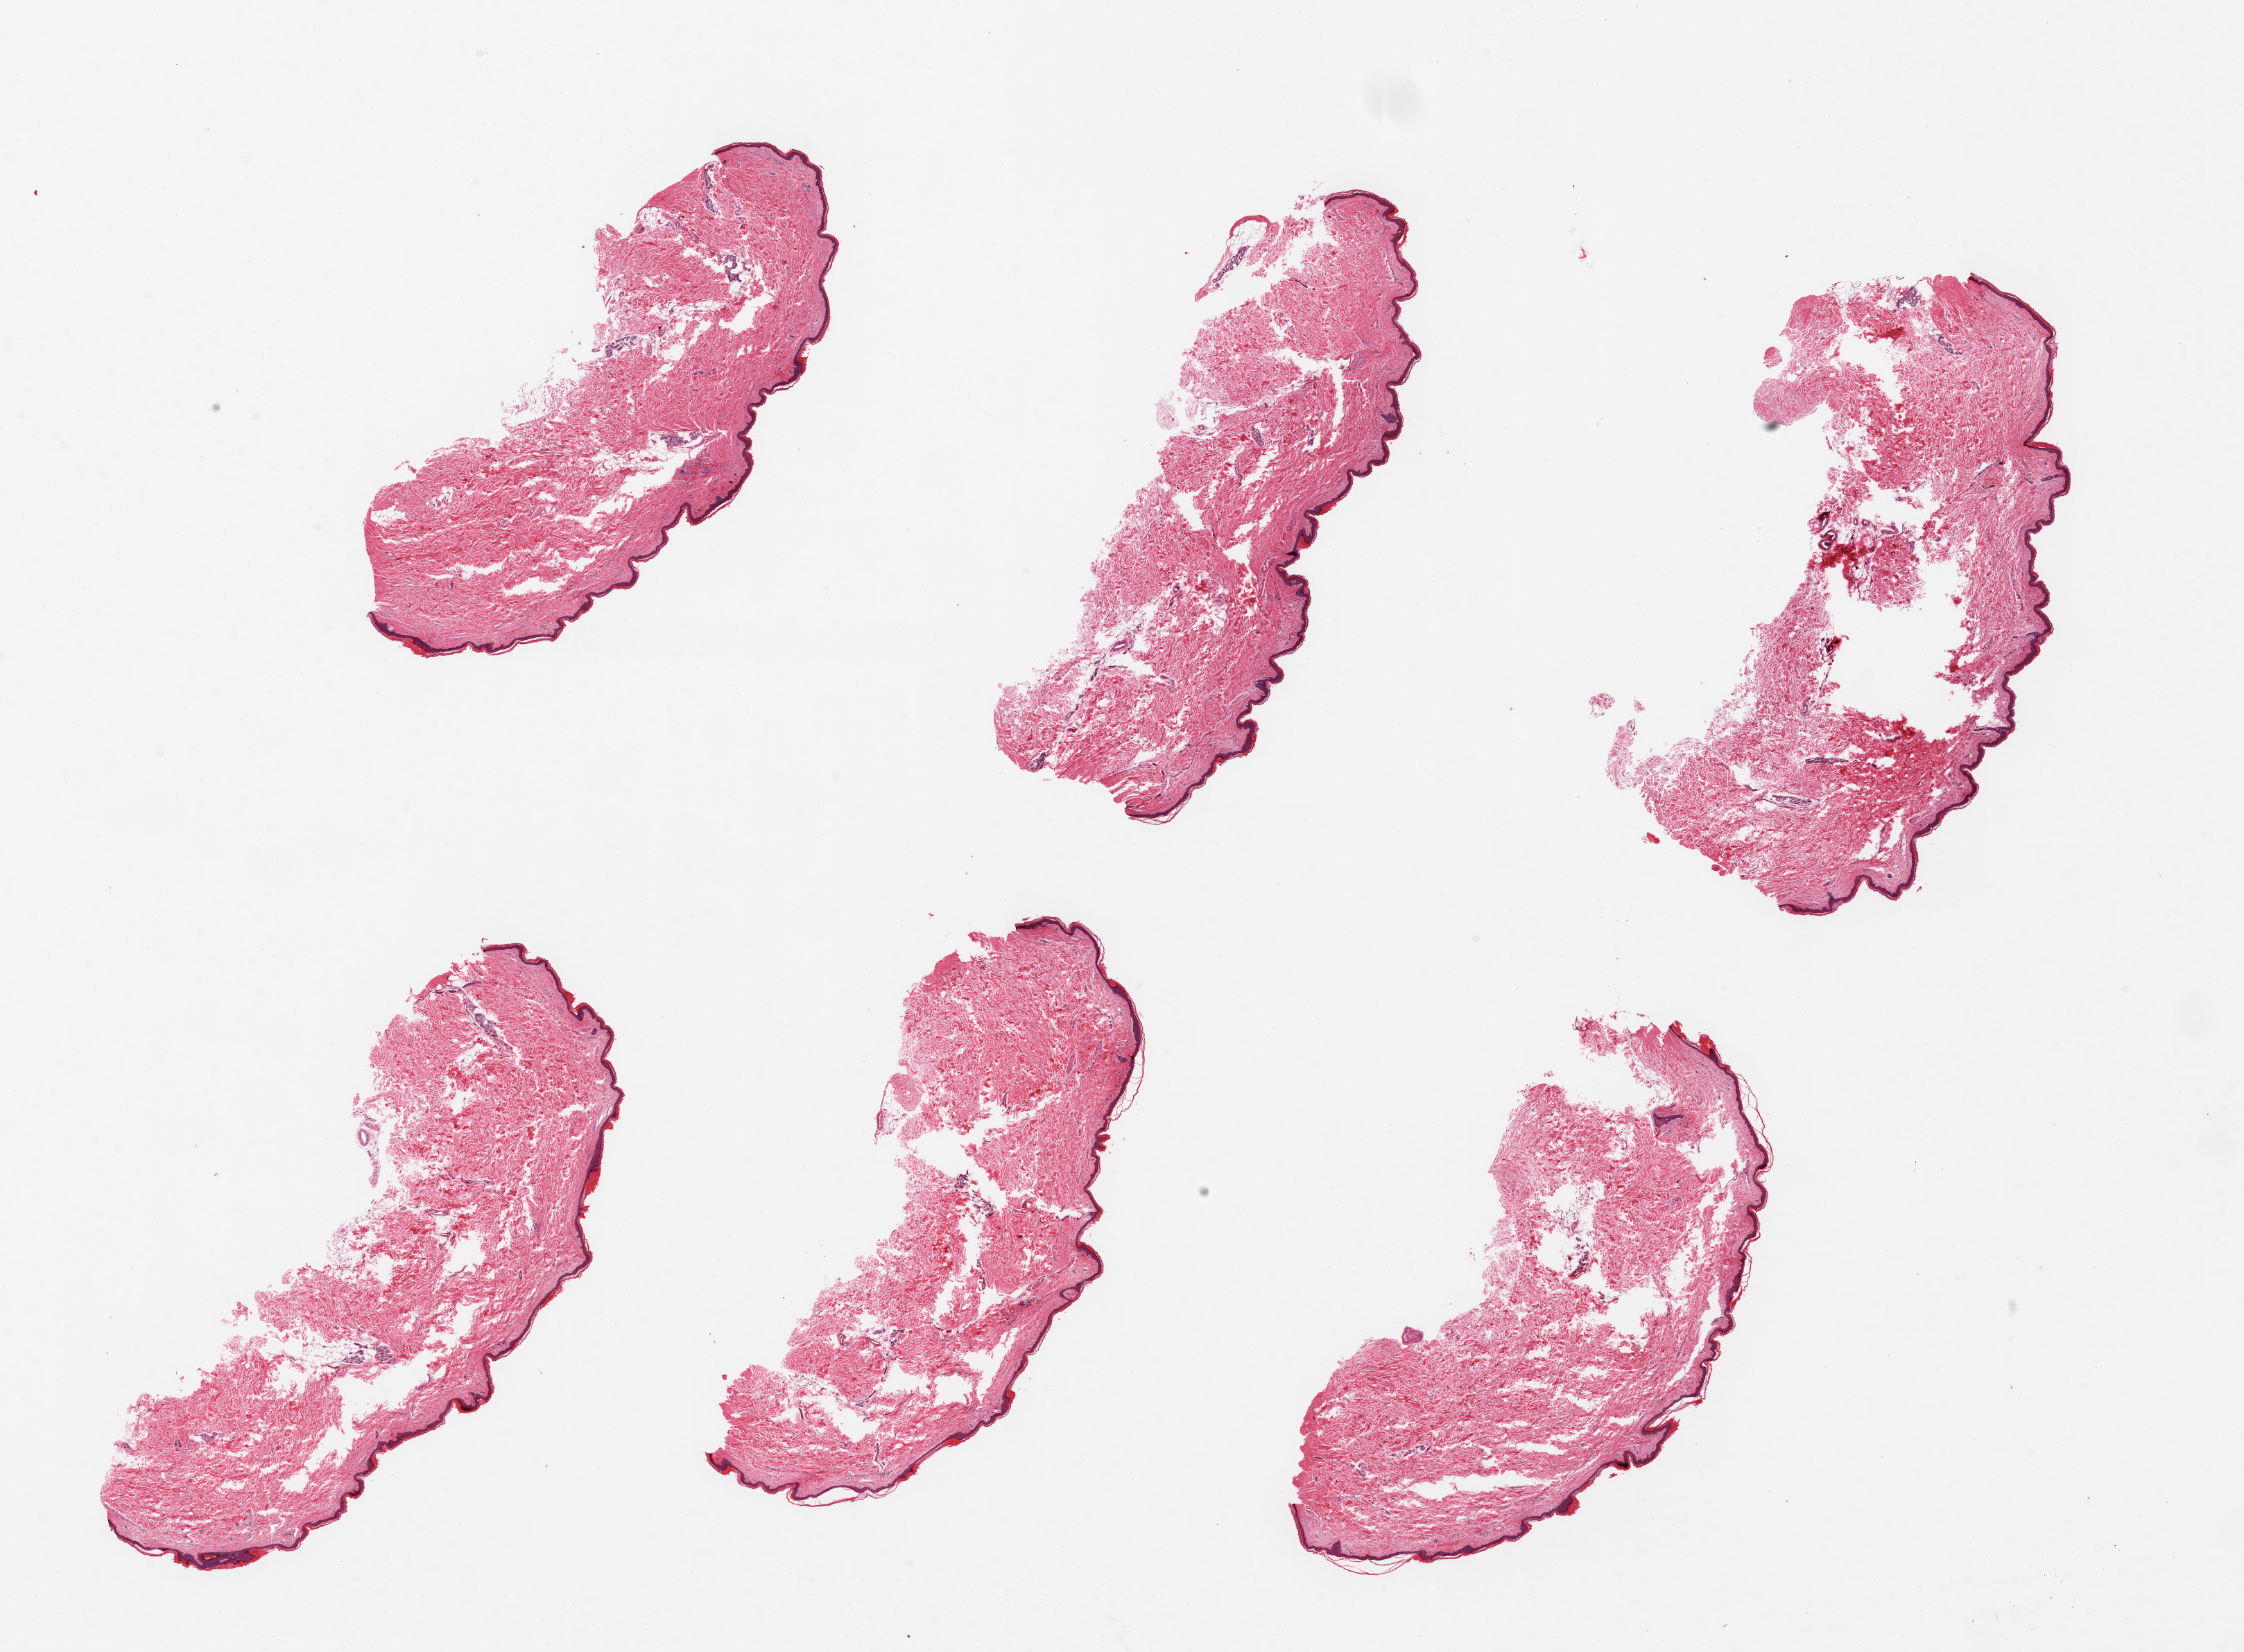
Digitized H&E-stained section, shown as a low-resolution overview of the whole scanned area (about 25.6 x 18.8 mm), PAXgene-fixed paraffin-embedded (PFPE) section, target tissue: skin of lower leg, donor tissue sample. Donor sex: female.
- review note (as recorded): 6 pieces up to 8x3 mm; subcutaneous fat well trimmed; numerous tissue fractures in dermis